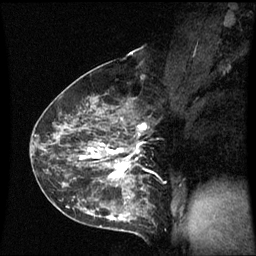
Breast MRI (dynamic contrast-enhanced), one sagittal slice; position 35 of 60 along the scan axis; dynamic contrast-enhanced series, image 2 of 3 at this slice position (ordered by acquisition); 1.5 T; TE 4.2 ms, TR 8.9 ms; 2.3 mm slice thickness; 256 × 256 image matrix, field of view 210 × 210 mm. Patient: female, 43 years. From the clinical record (not read from this slice): setting: breast cancer imaged before/during neoadjuvant chemotherapy; receptor status: HER2-positive.
Structures marked on this image (semi-automatically segmented with operator editing):
- analysis volume of interest (the breast-tissue region the enhancement analysis was run in; not a lesion): bounding box <56,80,148,195> (left, top, right, bottom; pixels)
- tumour enhancement mask (voxels above the 70 % enhancement threshold inside the analysis volume of interest): <81,119,146,179>